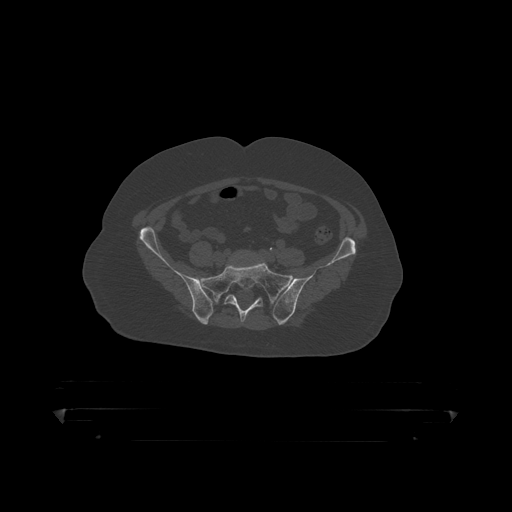
CT including the spine, one axial slice. Reconstruction kernel STANDARD. 120 kVp. Bone window (W 1800 / L 400 HU). 1.25 mm slice thickness. 512 × 512 image matrix. Patient: male, 60 years. From the clinical record (not read from this slice): primary cancer: prostate.
Annotated regions visible in this slice (semi-automatically segmented with operator editing):
- L5 vertebra: bounding box <231,250,258,257> (left, top, right, bottom; pixels)